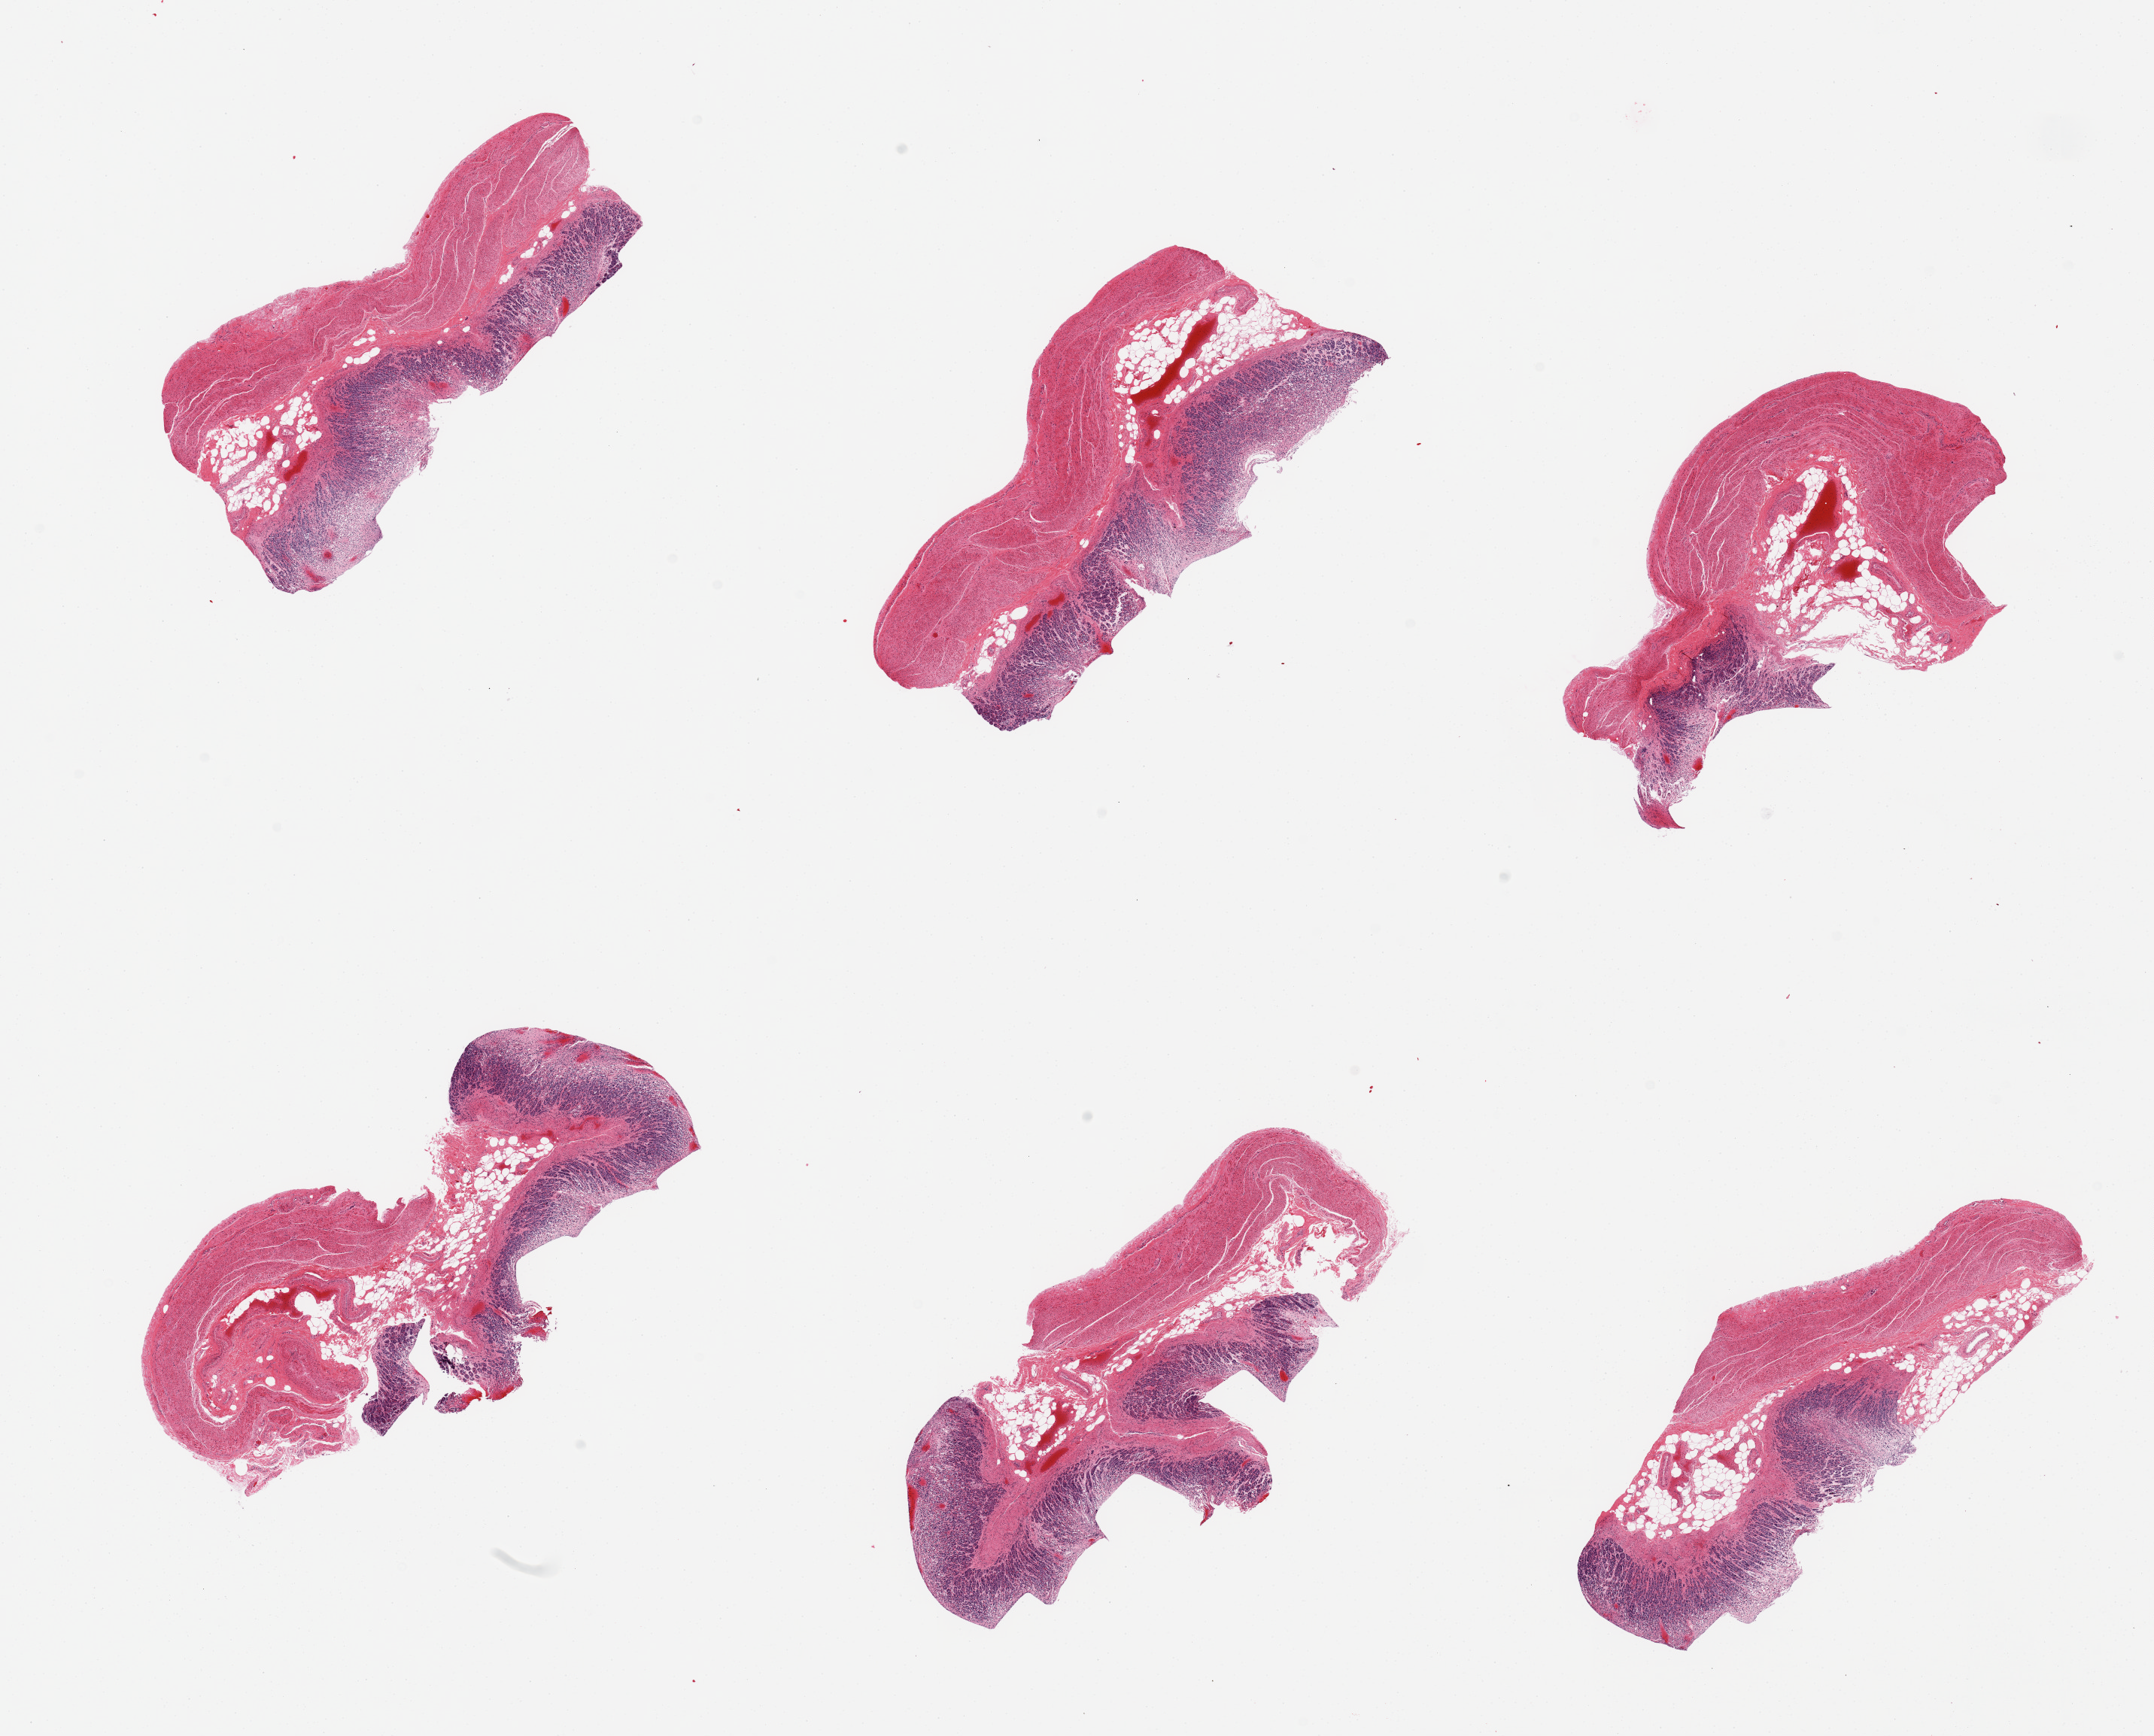
H&E whole-slide image, brightfield, a low-resolution overview of the entire scanned area, about 22.6 x 18.3 mm (from a 20x scan), PAXgene-fixed paraffin-embedded (PFPE) section, sampled site (target tissue): stomach, donor tissue sample.
* pathologist's review note for this sample: 6 pieces, severely autolyzed mucosa and muscularis